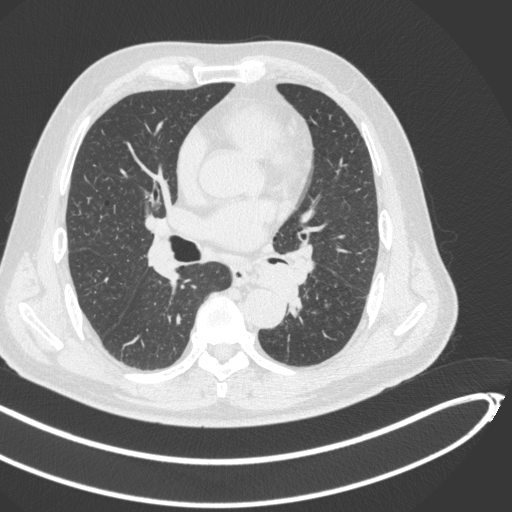
Chest CT, one axial slice. Position 248 of 466 along the scan axis. Lung window (W 1500 / L -600 HU). 512 × 512 image matrix, field of view 400 × 400 mm. Patient: male, 64 years. From the clinical record (not read from this slice): clinical TNM (as recorded): T1c N0 M0.
Outlined on this slice (rectangle marked by the reading radiologist):
- lung tumour (recorded histology: squamous cell carcinoma): box from (x=252, y=258) to (x=303, y=313) px